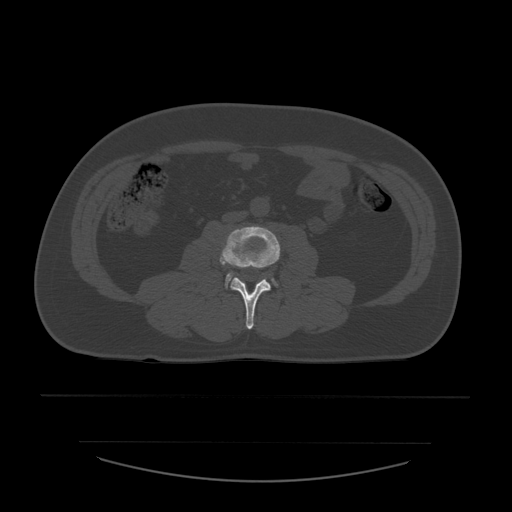
CT including the spine, one axial slice; 120 kVp; bone window (W 1800 / L 400 HU); 1.25 mm slice thickness; 512 × 512 image matrix, field of view 441 × 441 mm. Patient age 44 years. Case-level facts recorded for this patient, not image findings: primary cancer: soft tissue sarcoma.
Outlined on this slice (semi-automatic segmentation, software-assisted and operator-edited):
- L3 vertebra: box from (x=220, y=226) to (x=281, y=330) px
- L4 vertebra: (x=226, y=274)–(x=276, y=287)